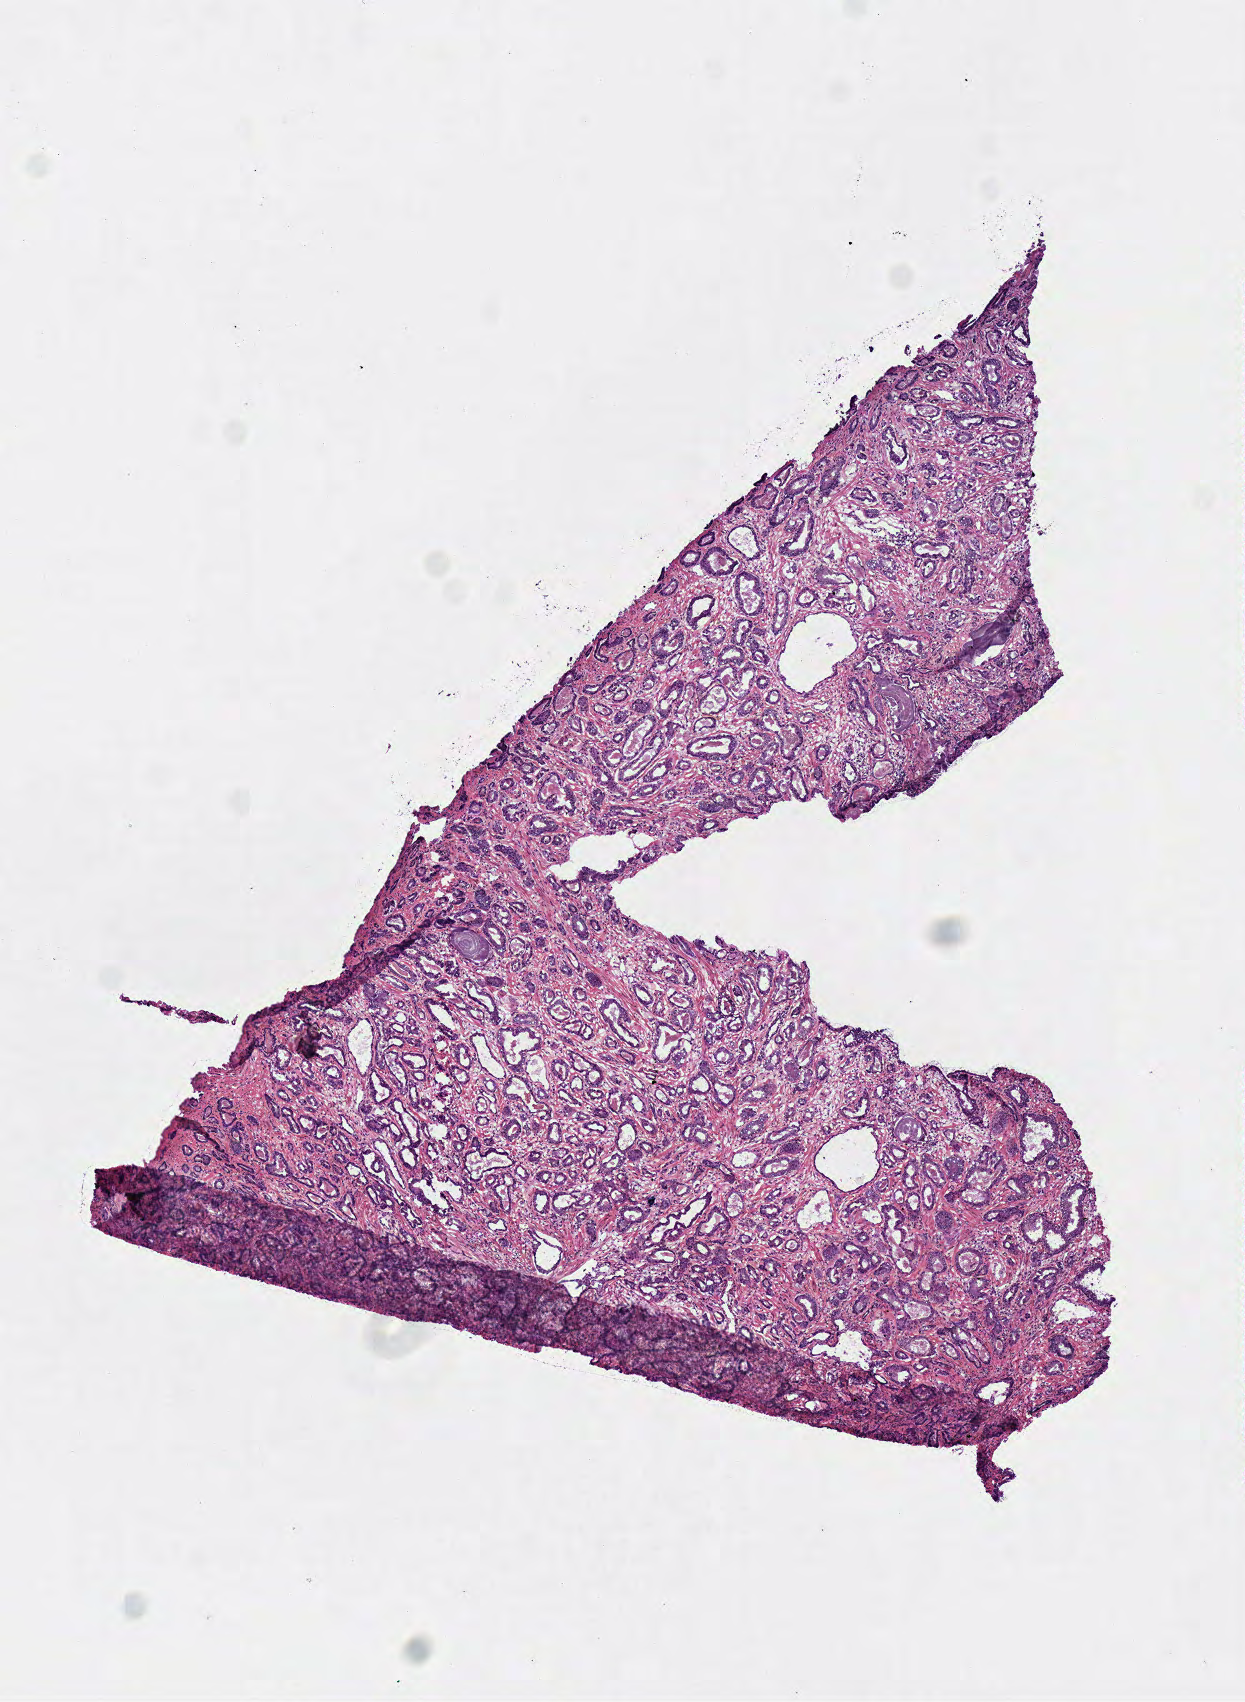
Whole-slide histology image, H&E, low-resolution overview of the scanned area, about 4.9 x 6.7 mm (from a 40x scan). Frozen section from the top of the tissue portion. Primary tumour sample from the prostate. Male, age 57 years at initial diagnosis.
Diagnosis: Acinar cell carcinoma (prostate gland).